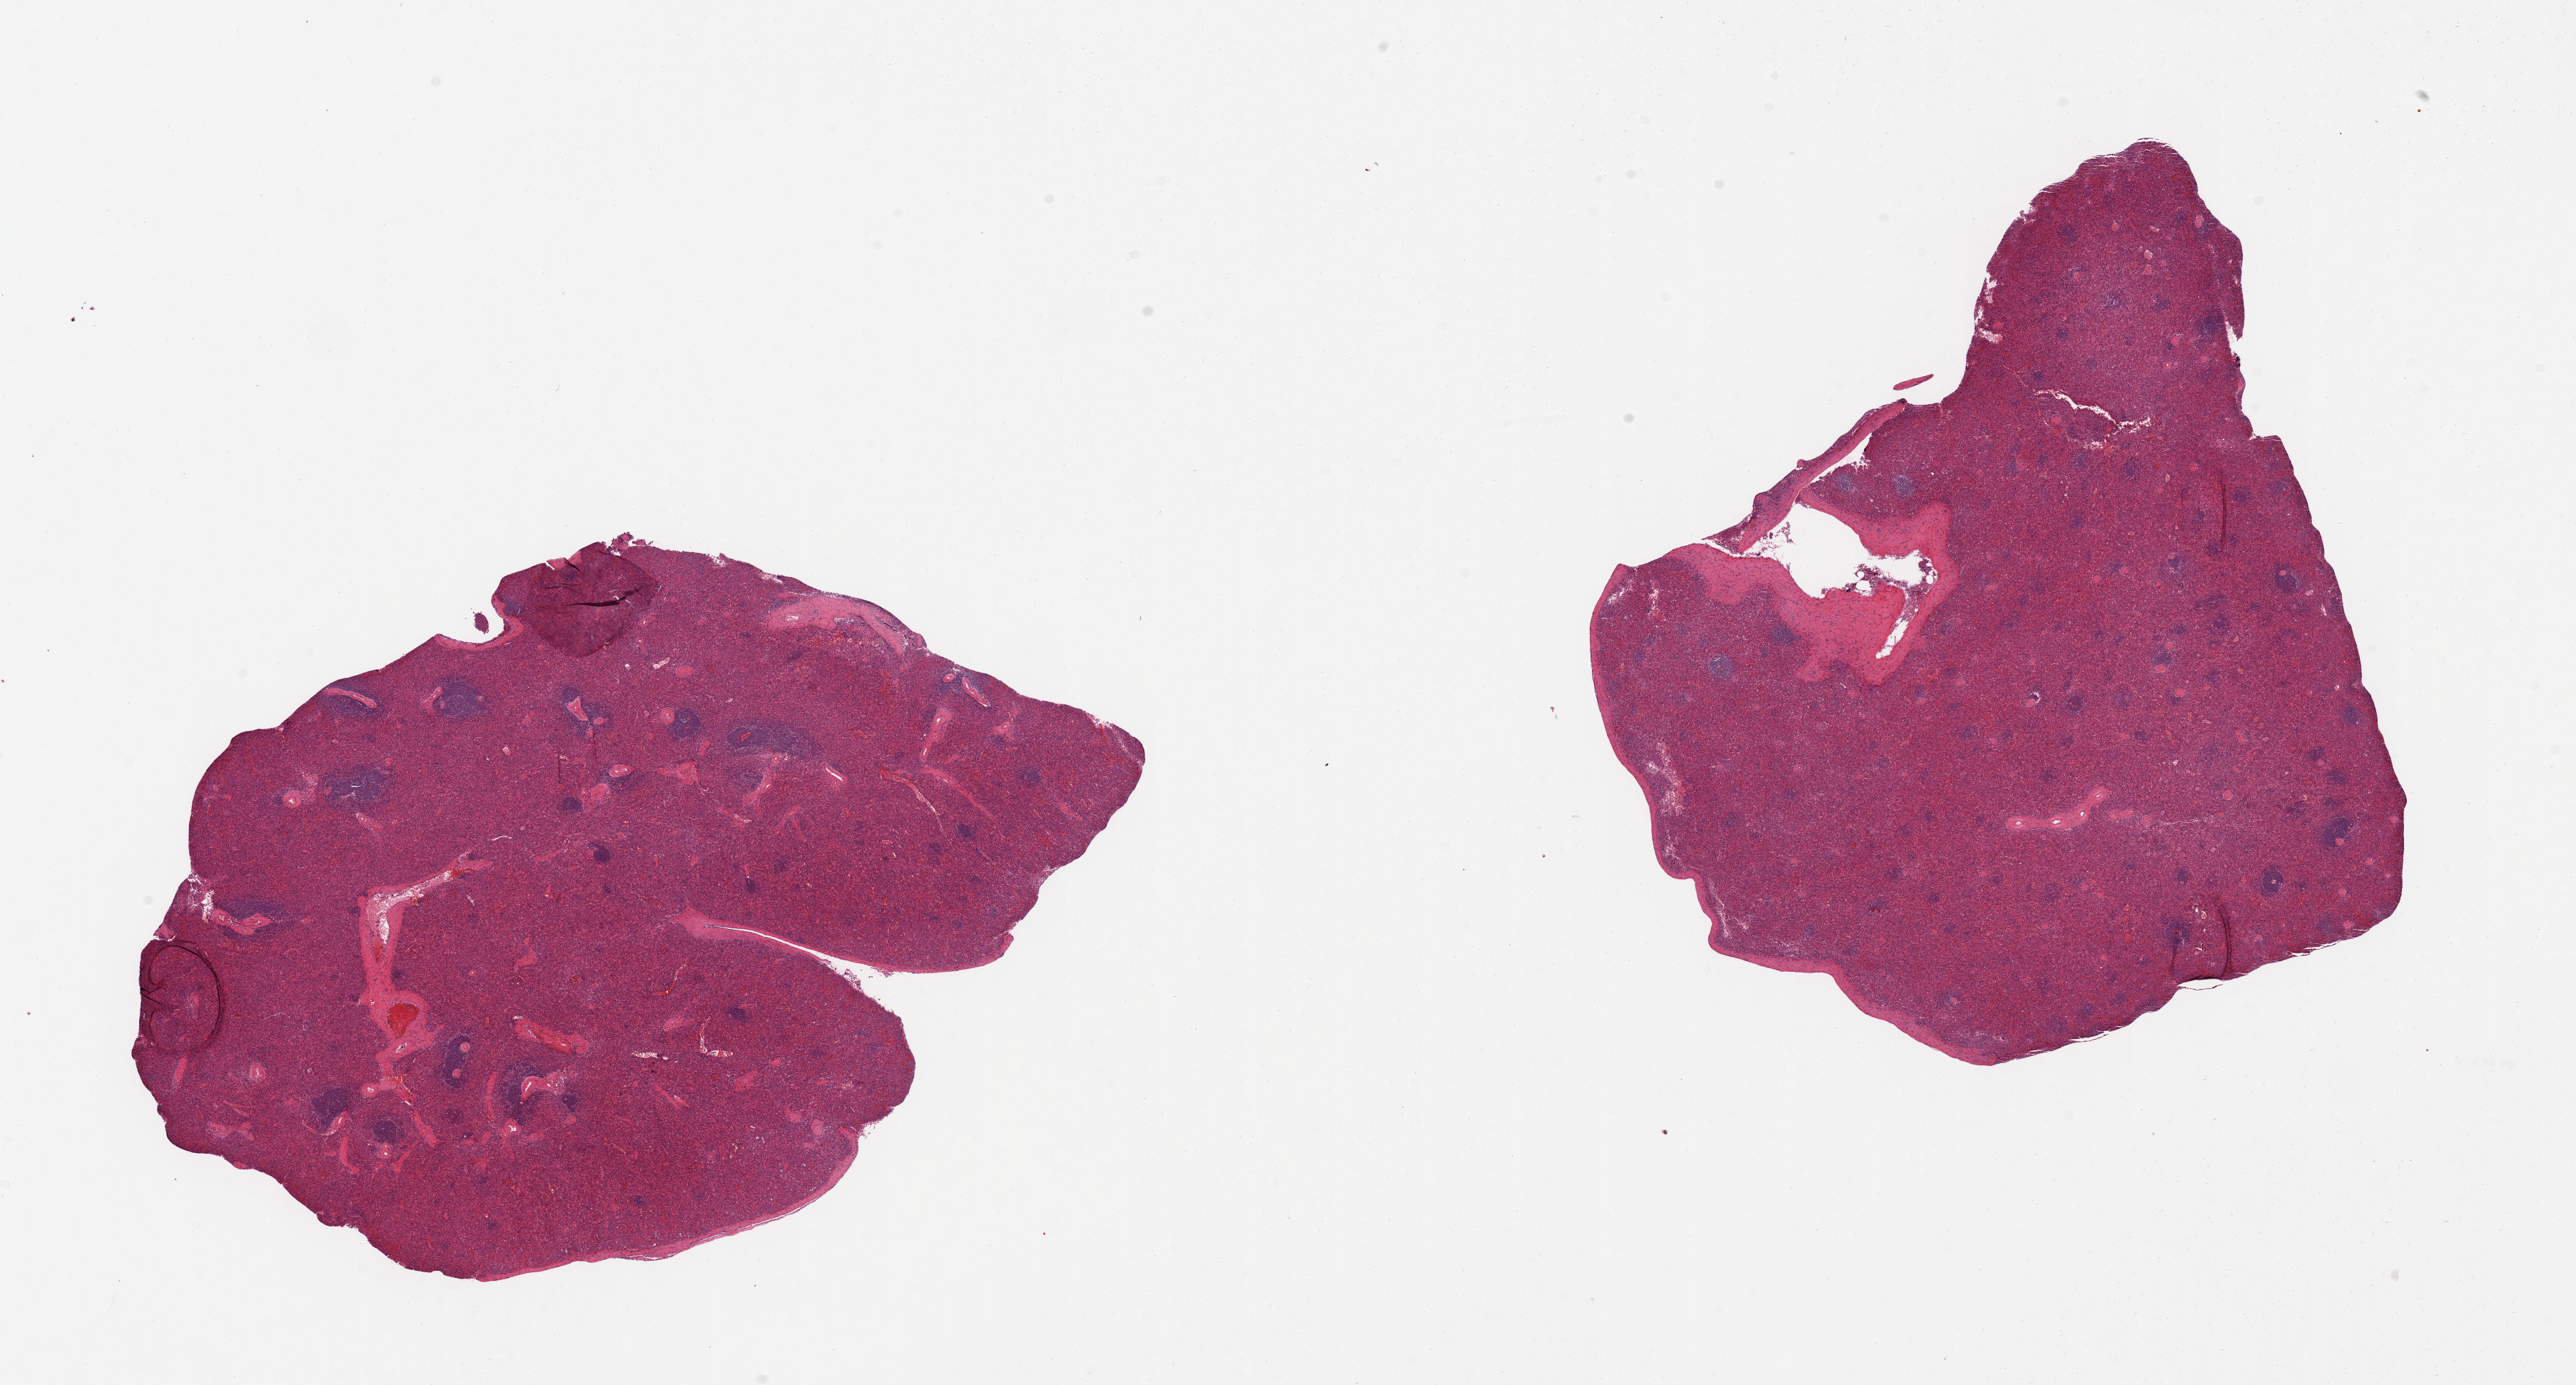
Whole-slide image, hematoxylin and eosin (H&E) stain — a low-resolution overview of the entire scanned area, about 28.5 x 15.3 mm (from a 20x scan). PAXgene-fixed, paraffin-embedded tissue. Sampled site (target tissue): spleen. Tissue donor sample. Female donor.
Pathologist's review note for this sample: 2 pieces, some congestion.